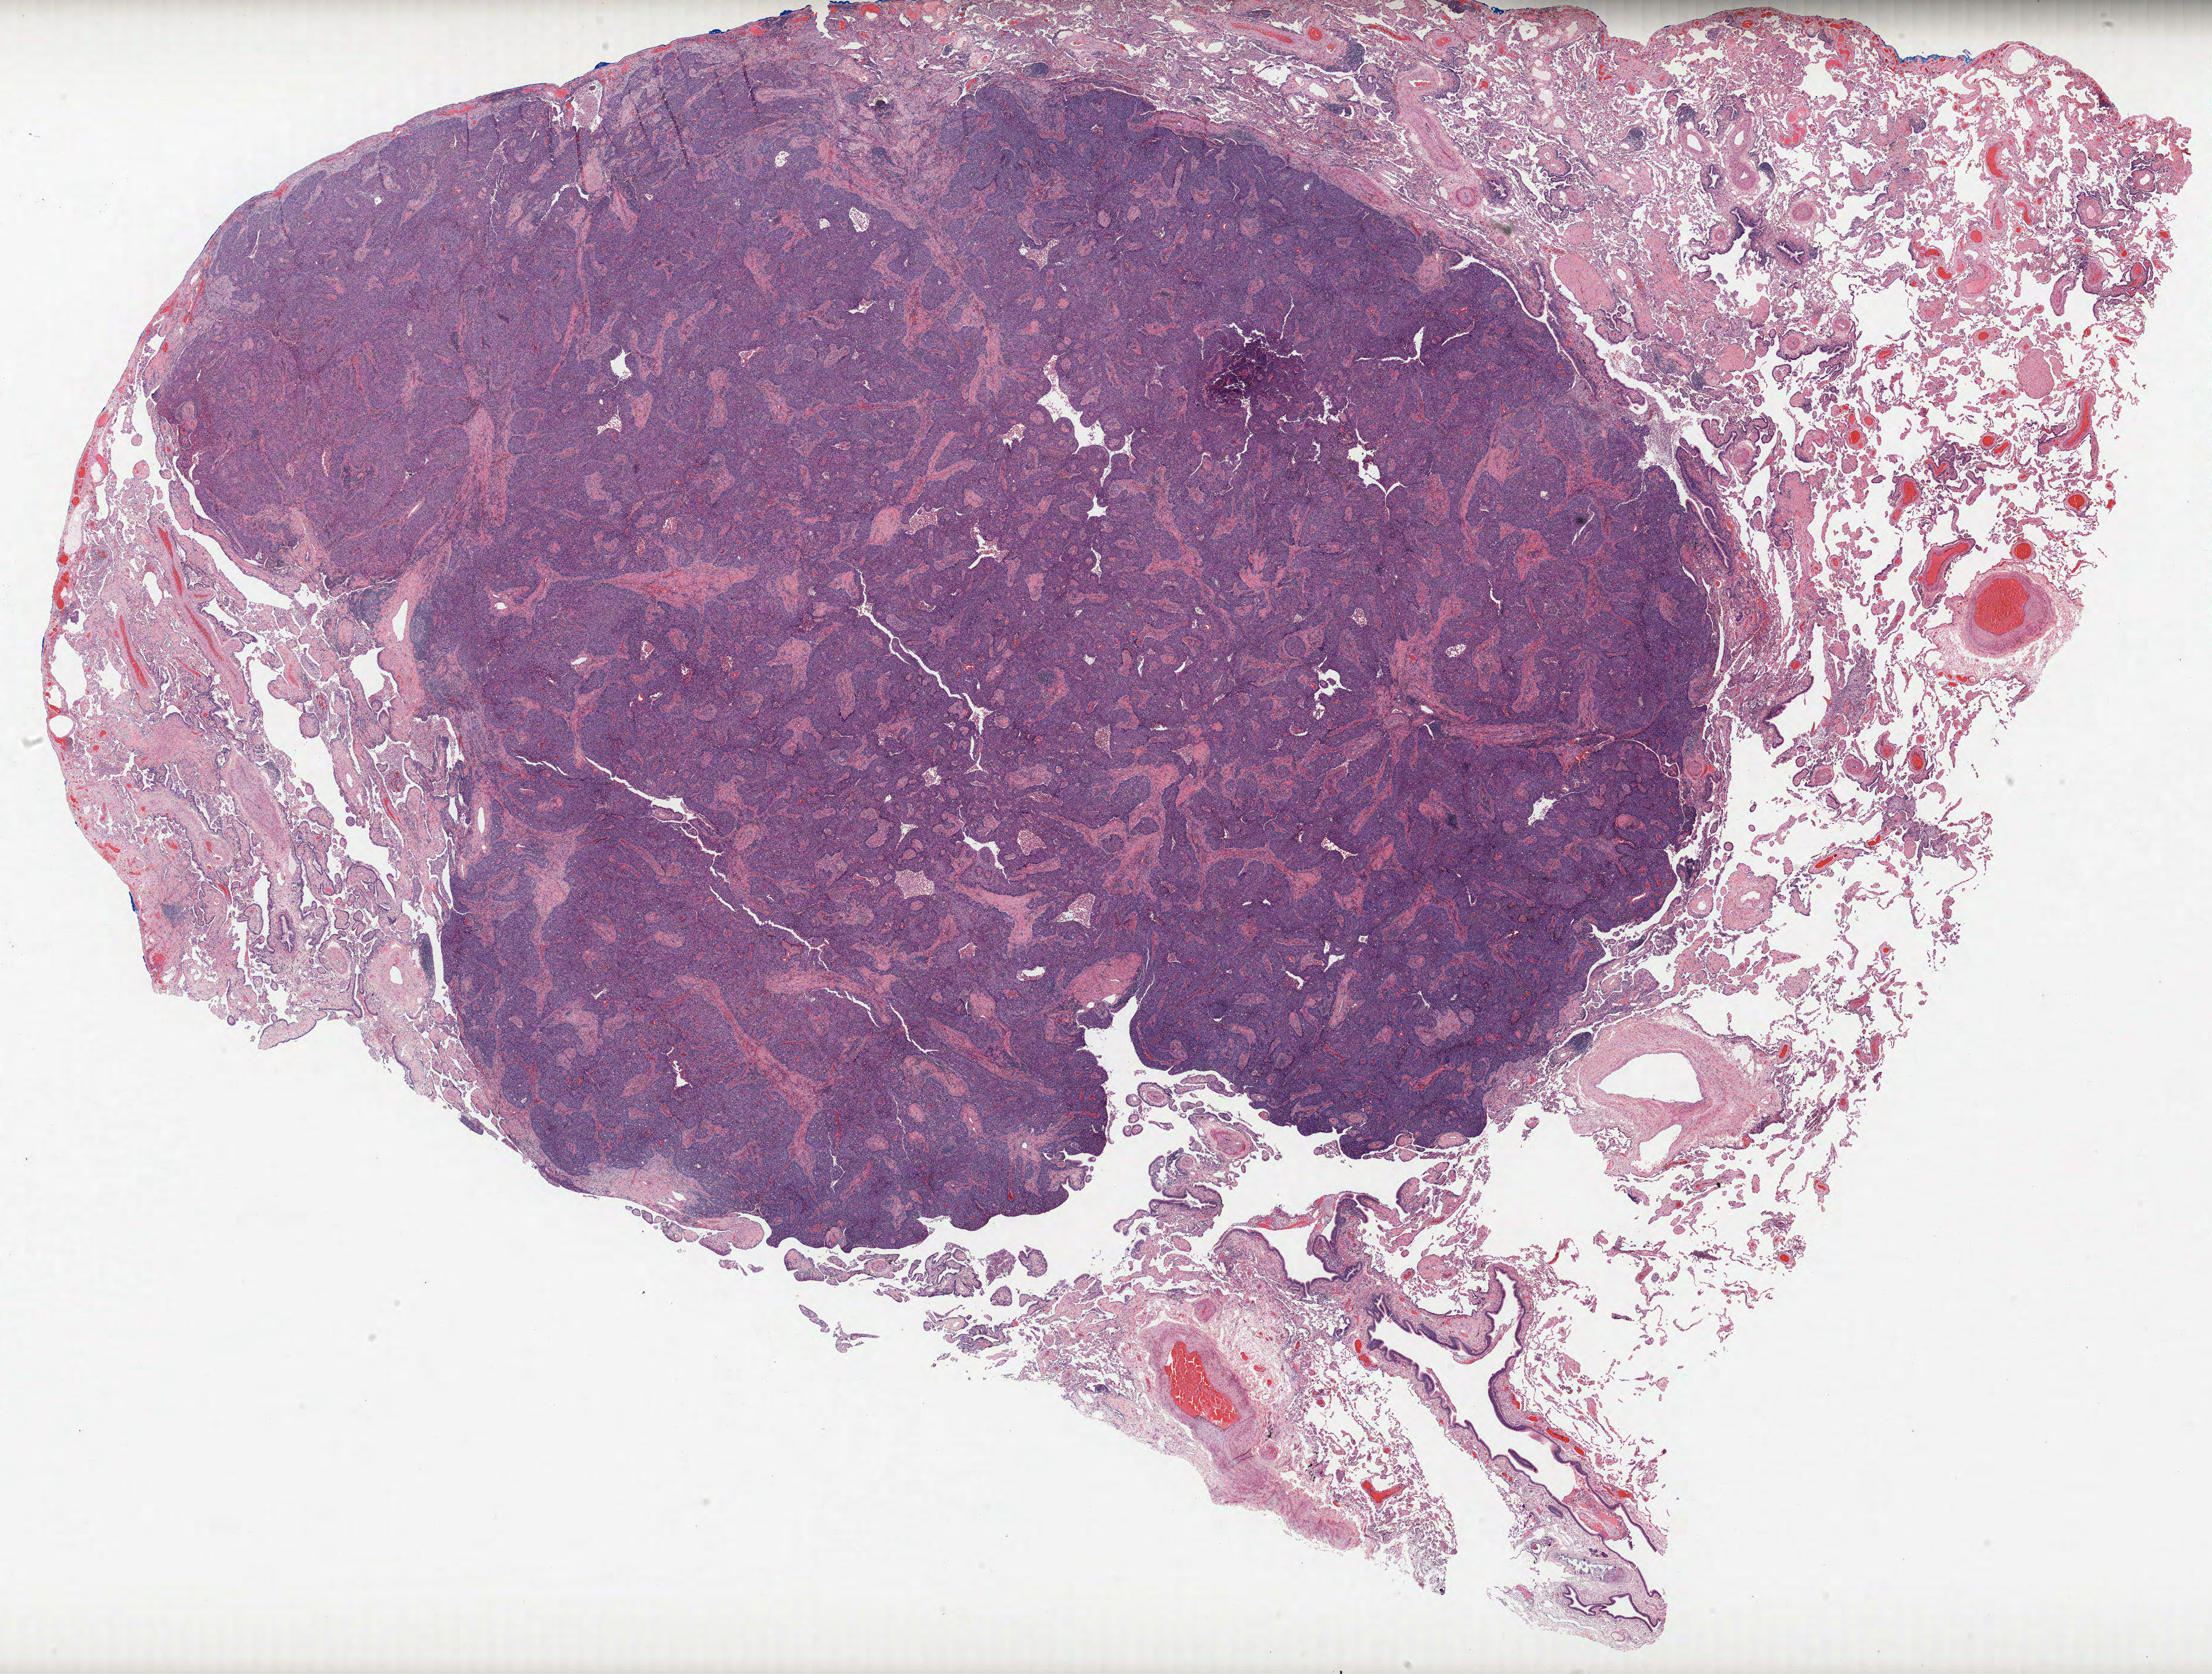
H&E-stained whole-slide image — whole scanned area (about 29.5 x 22.3 mm, acquisition: 40x scan) shown as a low-resolution overview. Formalin-fixed paraffin-embedded (FFPE) section. Lung. Male, age 68 at enrolment. Grade: poorly differentiated (G3).
• tumour size (pathology): 45 mm
• participant's lung-cancer diagnosis: Squamous cell carcinoma, NOS
• stage (AJCC 6th edition): IB
• primary tumour location (clinical record): right lower lobe